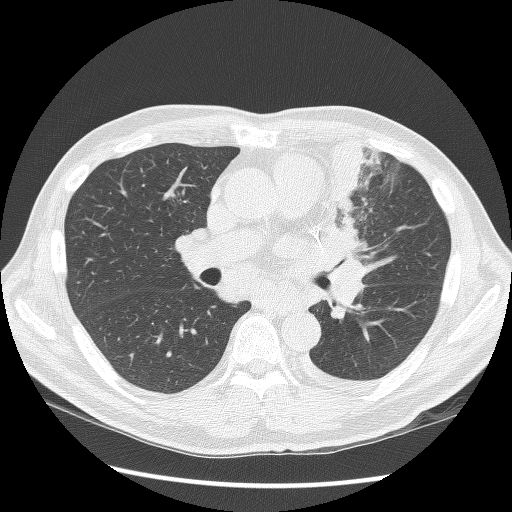
Axial slice from a low-dose chest CT screening exam. Second screening round (one year after baseline). Lung window (W 1500 / L -600 HU). 2.5 mm slice thickness. Lung (sharp) reconstruction kernel (BONE). Slice 57 of 136 in the series. 512 × 512 image matrix, field of view 360 × 360 mm. Male participant, aged 64 years at enrolment.
• Expert reader's lesion annotation, bounding box <305,134,391,280> (left, top, right, bottom; pixels).
• No non-calcified nodule or mass ≥4 mm was recorded by the screening reader at this exam.
• Lung cancer was diagnosed 24 days after this screen: small cell carcinoma, NOS, left upper lobe, stage IV (AJCC 6th edition), 100 mm at pathology.